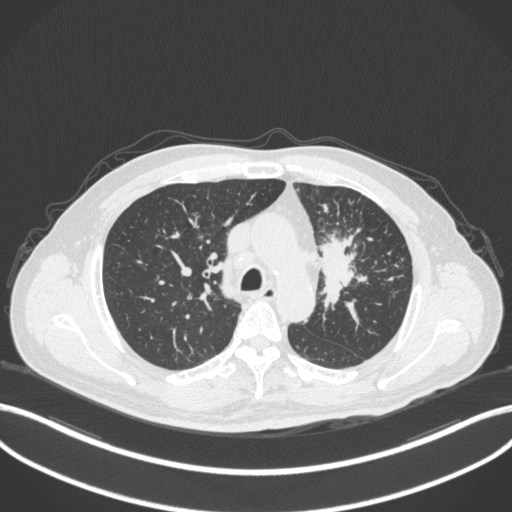
Chest CT, one axial slice. Position 245 of 386 along the scan axis. Reconstruction kernel B31f. Lung window (W 1500 / L -600 HU). 1 mm slice thickness. 512 × 512 image matrix. Patient: male, 69 years. Case-level facts recorded for this patient, not image findings: clinical TNM (as recorded): T2a N2 M0; histopathological grade: G2-3.
Structures marked on this image (rectangle marked by the reading radiologist):
- lung tumour (recorded histology: adenocarcinoma): box from (x=318, y=232) to (x=368, y=311) px